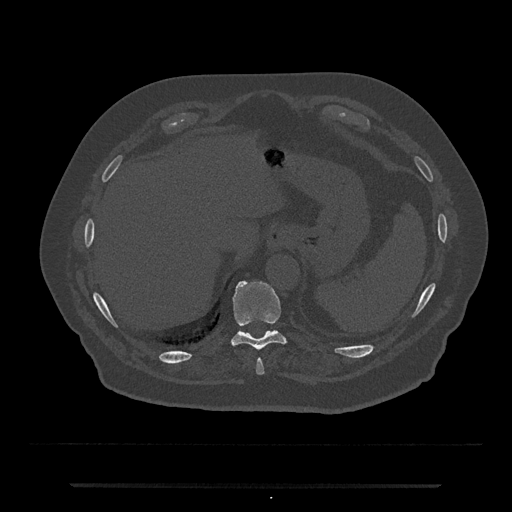
CT including the spine, one axial slice. Position 705 of 797 along the scan axis. Reconstruction kernel Br40s/3. Bone window (W 1800 / L 400 HU). 512 × 512 image matrix, field of view 434 × 434 mm. Male patient, age 80 years. Case-level facts recorded for this patient, not image findings: primary cancer: prostate.
Structures marked on this image (semi-automatically segmented with operator editing):
- T10 vertebra: bounding box [x1, y1, x2, y2] px = [232, 280, 286, 350]
- T9 vertebra: [256, 359, 264, 375]